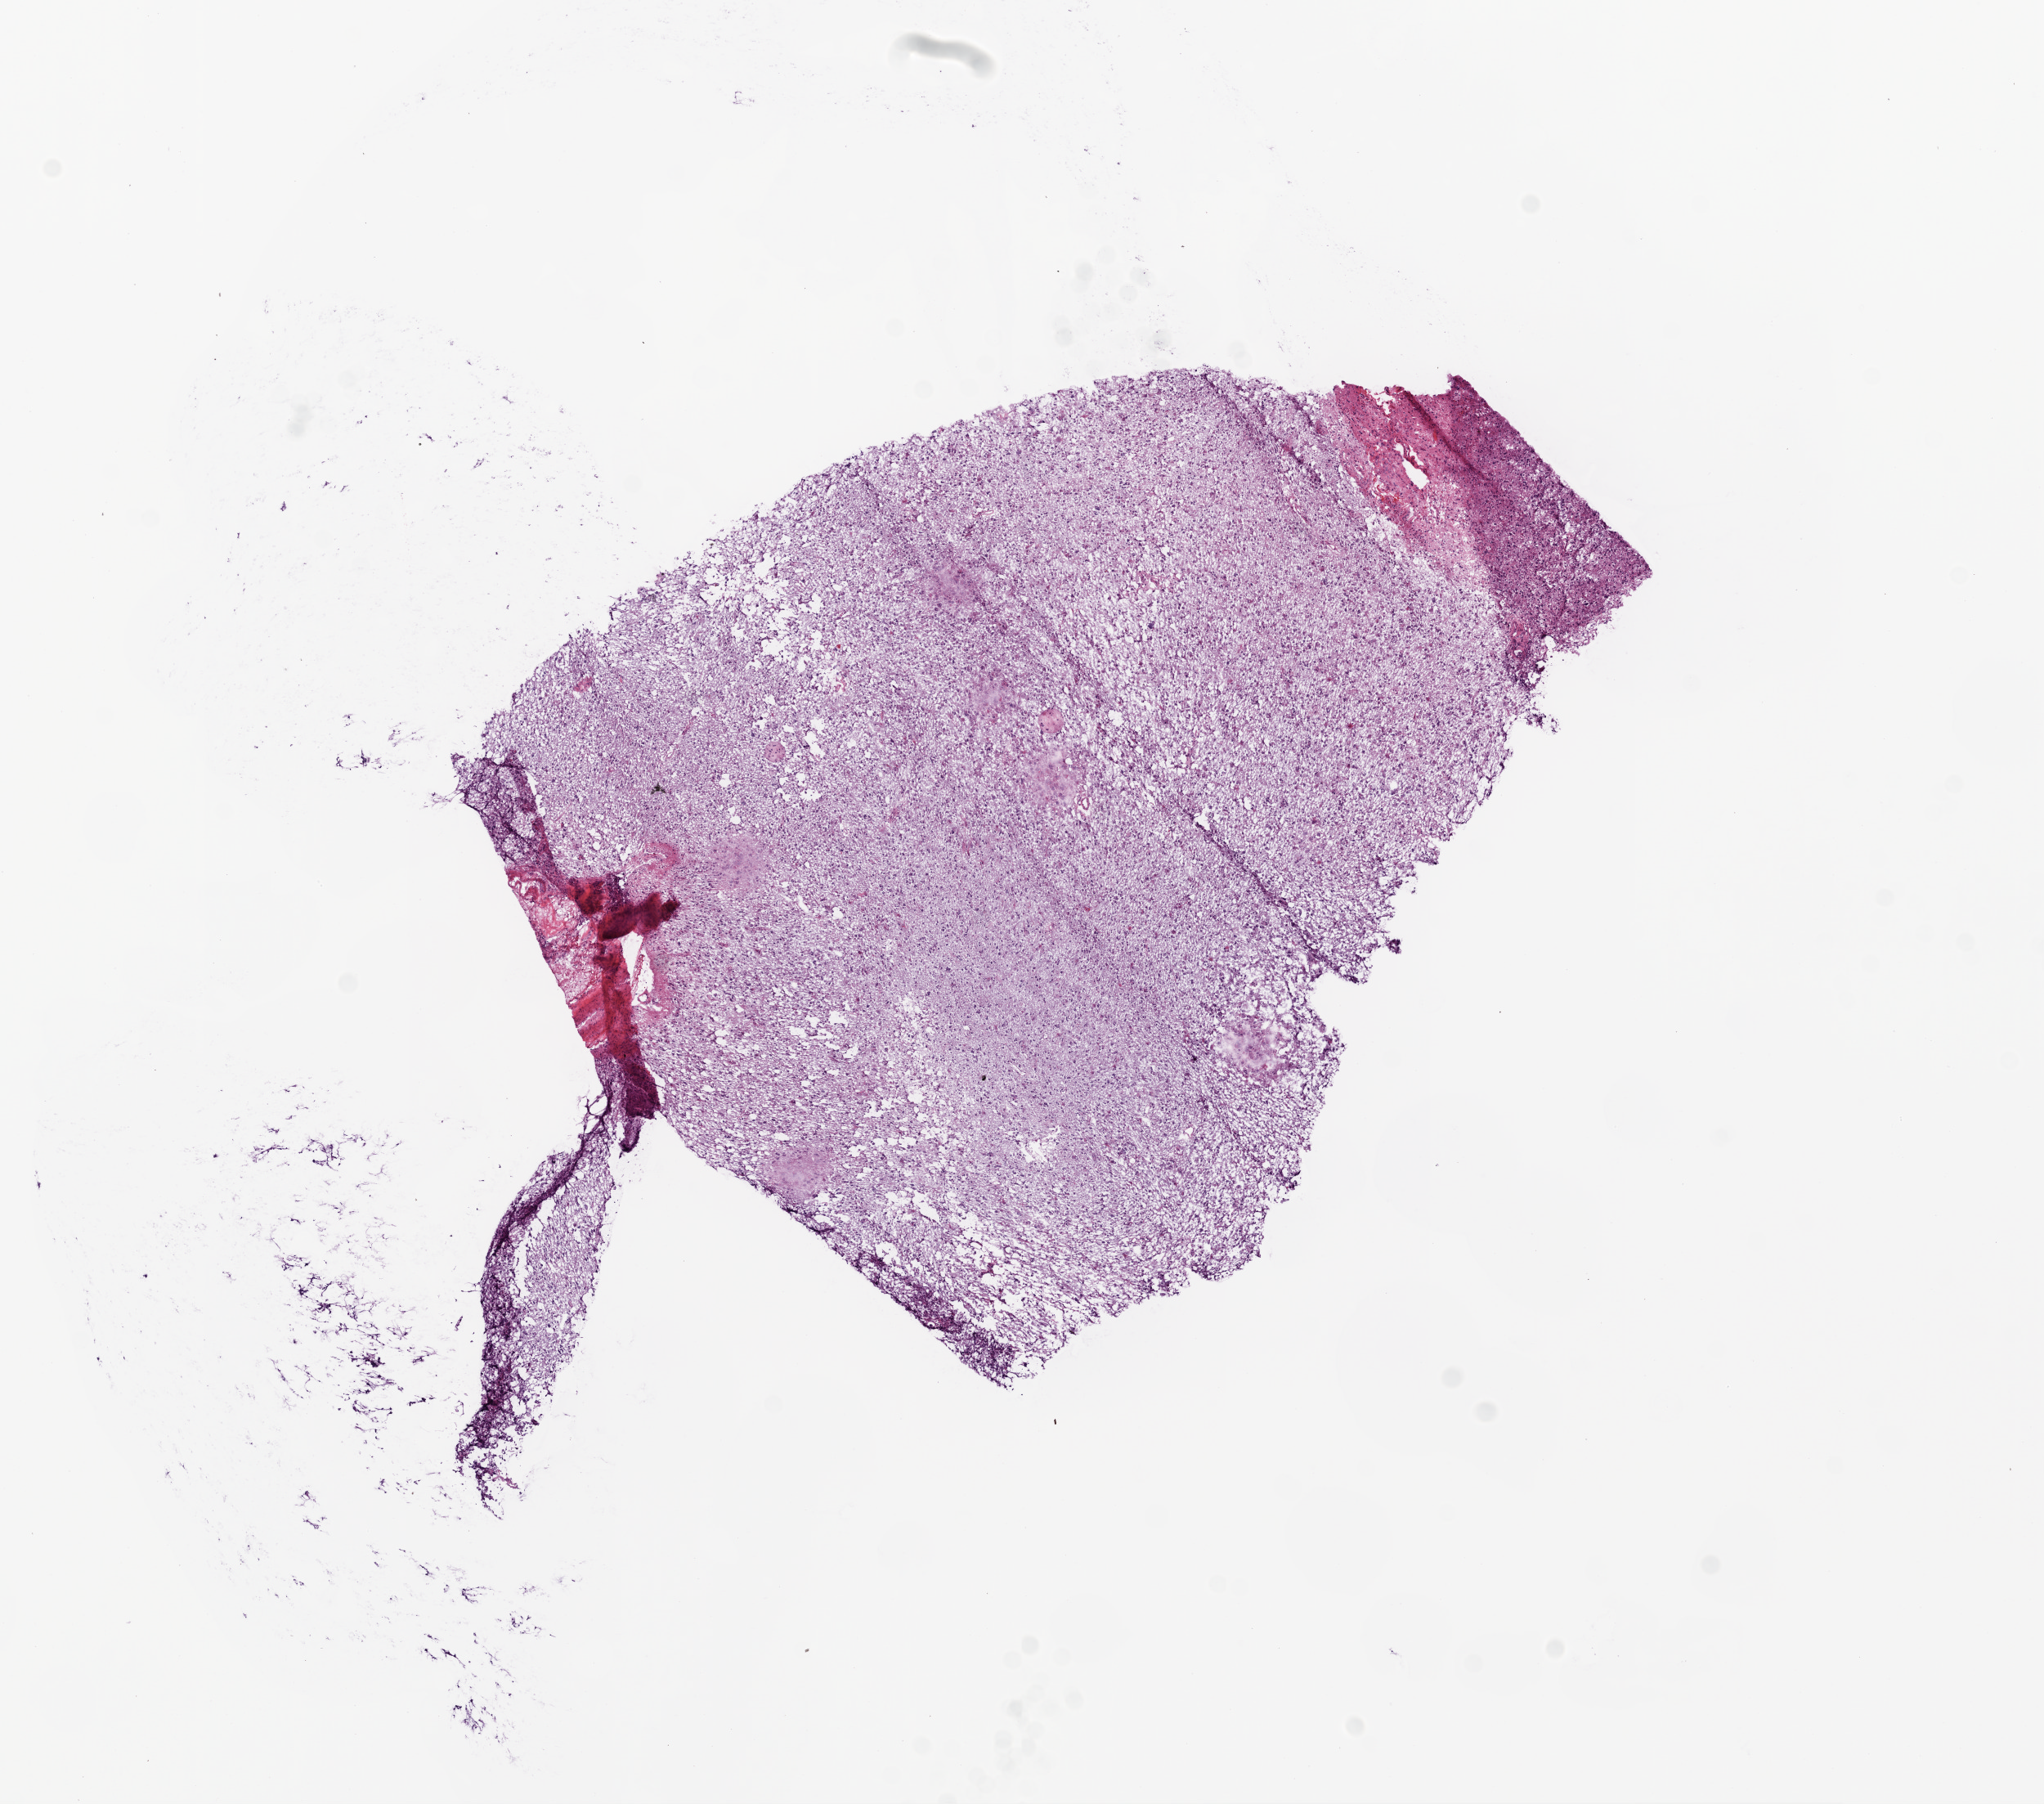
H&E whole-slide image, whole scanned area (about 10.0 x 8.9 mm) shown as a low-resolution overview. Frozen section from the top of the tissue portion. Sample: primary tumour, brain. Patient: male, age at initial diagnosis 78 years. Pathologist review of this section (percent, as recorded): tumour cells 100%, tumour nuclei 80%, normal cells 0%, stromal cells 0%, necrosis 0%.
Pathologic diagnosis: Glioblastoma.